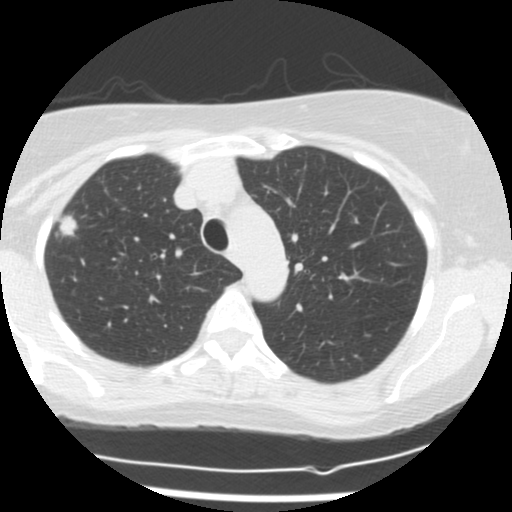
Axial slice from a low-dose chest CT screening exam; first (baseline) screen; lung window (W 1500 / L -600 HU); 2.5 mm slice thickness; standard (soft-tissue) reconstruction kernel (STANDARD); slice 42 of 160 in the series. Female, age 58 years at enrolment.
Expert-annotated lung lesion, bounding box (x1, y1, x2, y2) in pixels: (44, 205, 90, 242). Screening reader's record for this exam (one nodule recorded; not confirmed to be the boxed lesion): non-calcified nodule or mass ≥4 mm, right upper lobe, 12 × 9 mm, spiculated (stellate) margins, soft tissue attenuation. Lung cancer was diagnosed 21 days after this screen: adenocarcinoma, NOS, right upper lobe, moderately differentiated (G2), stage IA (AJCC 6th edition), 10 mm at pathology.